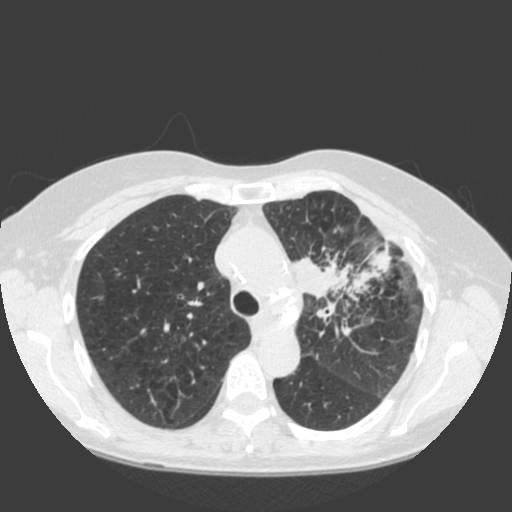
Low-dose screening chest CT, axial slice, baseline screening round, lung window (W 1500 / L -600 HU), 2 mm slice thickness, standard (soft-tissue) reconstruction kernel (C). Female participant, aged 66 years at enrolment. Current smoker at enrolment.
Lesion marked by an expert reader, bounding box [x1, y1, x2, y2] px = [285, 239, 397, 339]. Reader record for this screening exam (exam-level; its link to the box is not recorded): non-calcified nodule or mass ≥4 mm, left upper lobe, 61 × 45 mm, spiculated (stellate) margins, soft tissue attenuation. Lung cancer was diagnosed 19 days after this screen: squamous cell carcinoma, keratinizing, NOS, left upper lobe, left hilum, mediastinum, left main stem bronchus, other location, poorly differentiated (G3), stage IIIB (AJCC 6th edition), 60 mm at pathology.